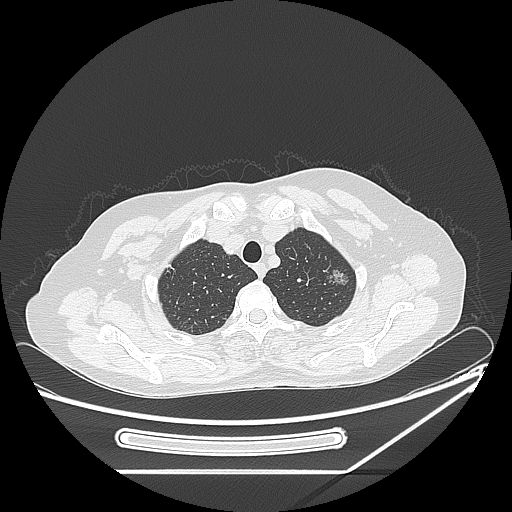
Chest CT, one axial slice; position 207 of 250 along the scan axis; reconstruction kernel LUNG; 120 kVp; lung window (W 1500 / L -600 HU); 512 × 512 image matrix, field of view 409 × 409 mm. Female patient, age 57 years. From the clinical record (not read from this slice): clinical TNM (as recorded): T1c N0 M0.
Outlined on this slice (bounding box drawn by a radiologist):
- lung tumour (recorded histology: adenocarcinoma): box from (x=326, y=263) to (x=347, y=289) px